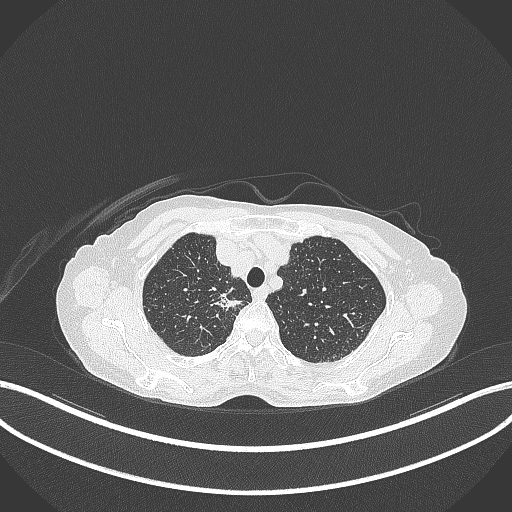
Chest CT, one axial slice; slice 305 of 403 in the series (ordered by position); reconstruction kernel B70f; 120 kVp; lung window (W 1500 / L -600 HU); 1 mm slice thickness; 512 × 512 image matrix, field of view 400 × 400 mm. Female patient, age 75 years. From the clinical record (not read from this slice): clinical TNM (as recorded): T1c N1 M1.
Outlined on this slice (bounding box drawn by a radiologist):
- lung tumour (recorded histology: adenocarcinoma): bounding box [x1, y1, x2, y2] px = [212, 286, 246, 311]